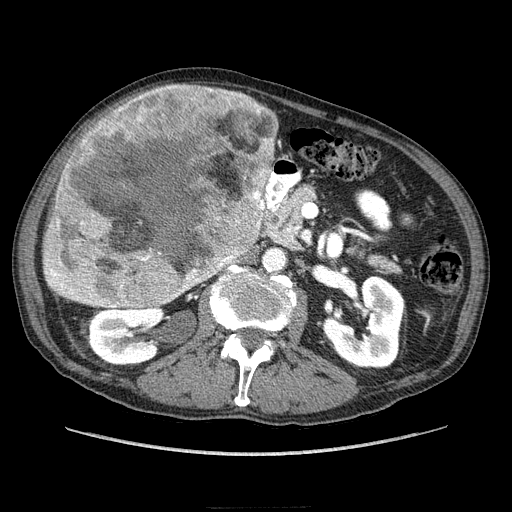
Contrast-enhanced abdominal CT (liver protocol), one axial slice. Slice 105 of 218 in the series (ordered by position). 100 kVp. Soft-tissue window (W 400 / L 40 HU). 512 × 512 image matrix, field of view 380 × 380 mm. From the clinical record (not read from this slice): diagnosis: hepatocellular carcinoma (patient treated with transarterial chemoembolisation; whether this scan precedes or follows treatment is not stated here); TNM stage (as recorded): Stage-IIIA; Child-Pugh class: A; tumour differentiation: well differentiated; tumour size: 20 cm.
Outlined on this slice (semi-automatically segmented with operator editing):
- mass: box from (x=40, y=83) to (x=277, y=312) px